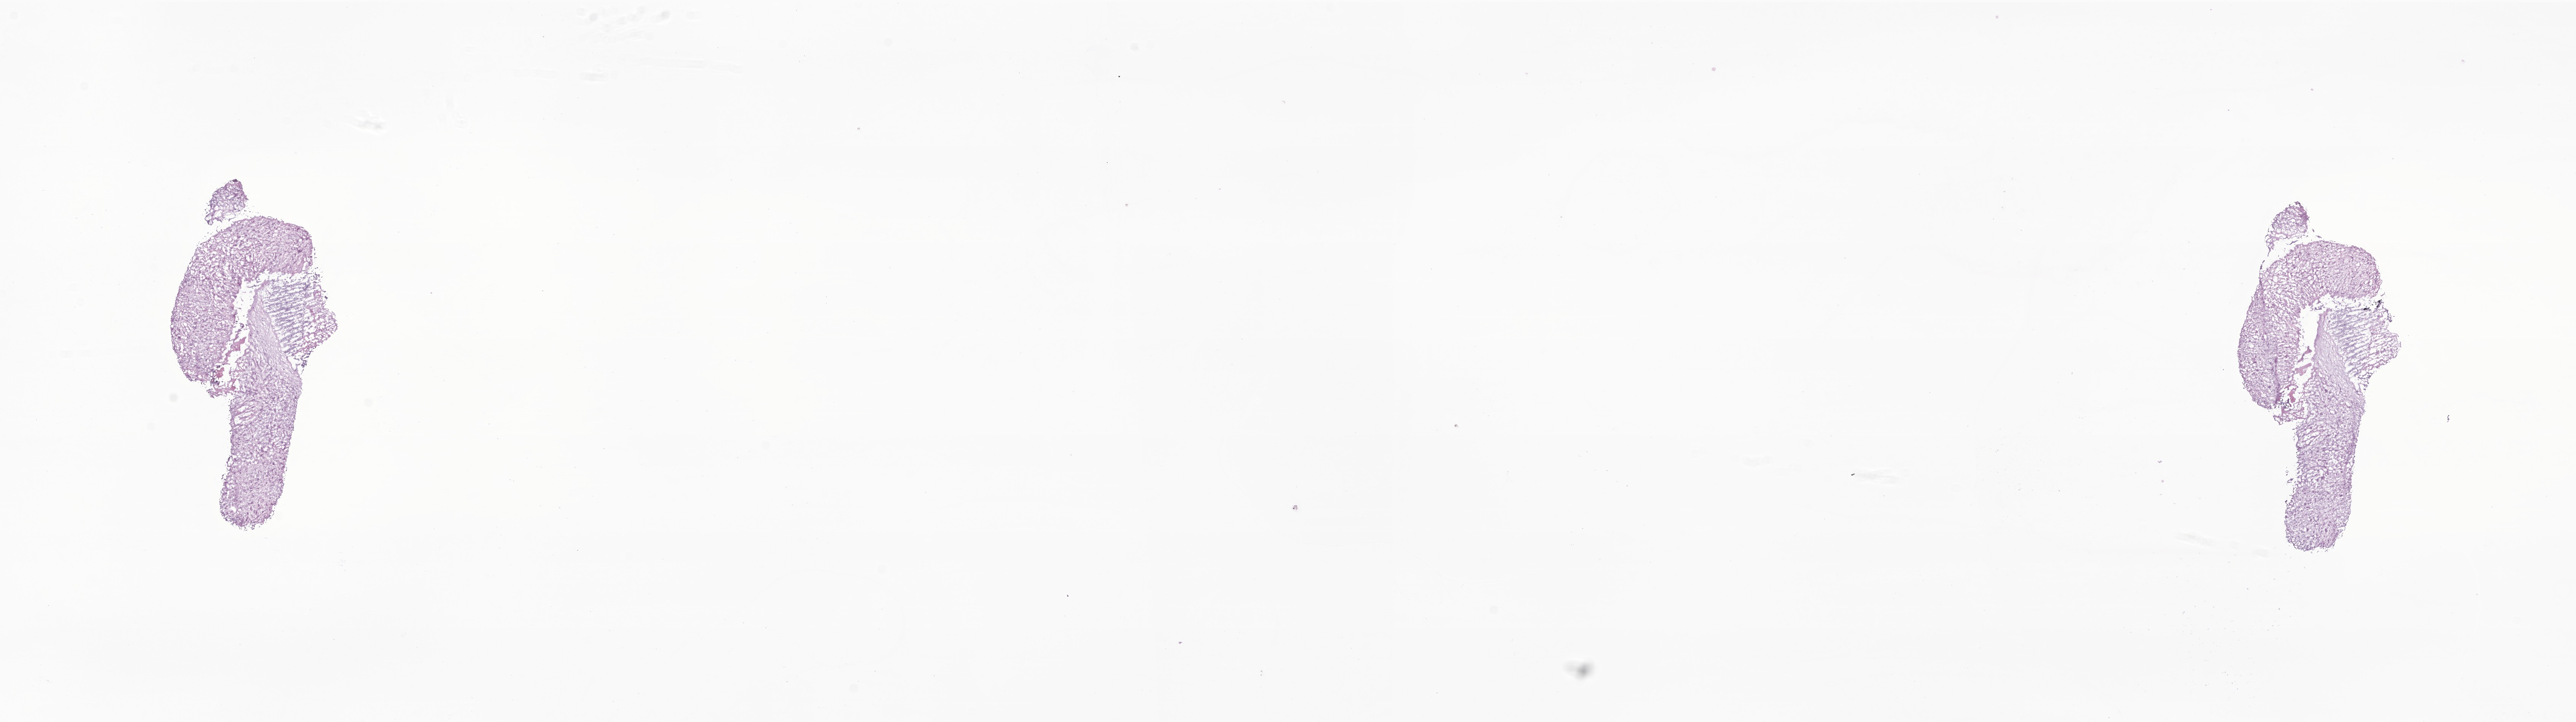
H&E whole-slide image of tumor tissue from the liver — shown as a low-resolution overview of the whole scanned area (about 28.5 x 8.0 mm). Frozen section (OCT-embedded). Male patient, age 493 days (about 1.3 years).
* diagnosis (ICD-O-3 morphology term): Rhabdoid tumor, NOS